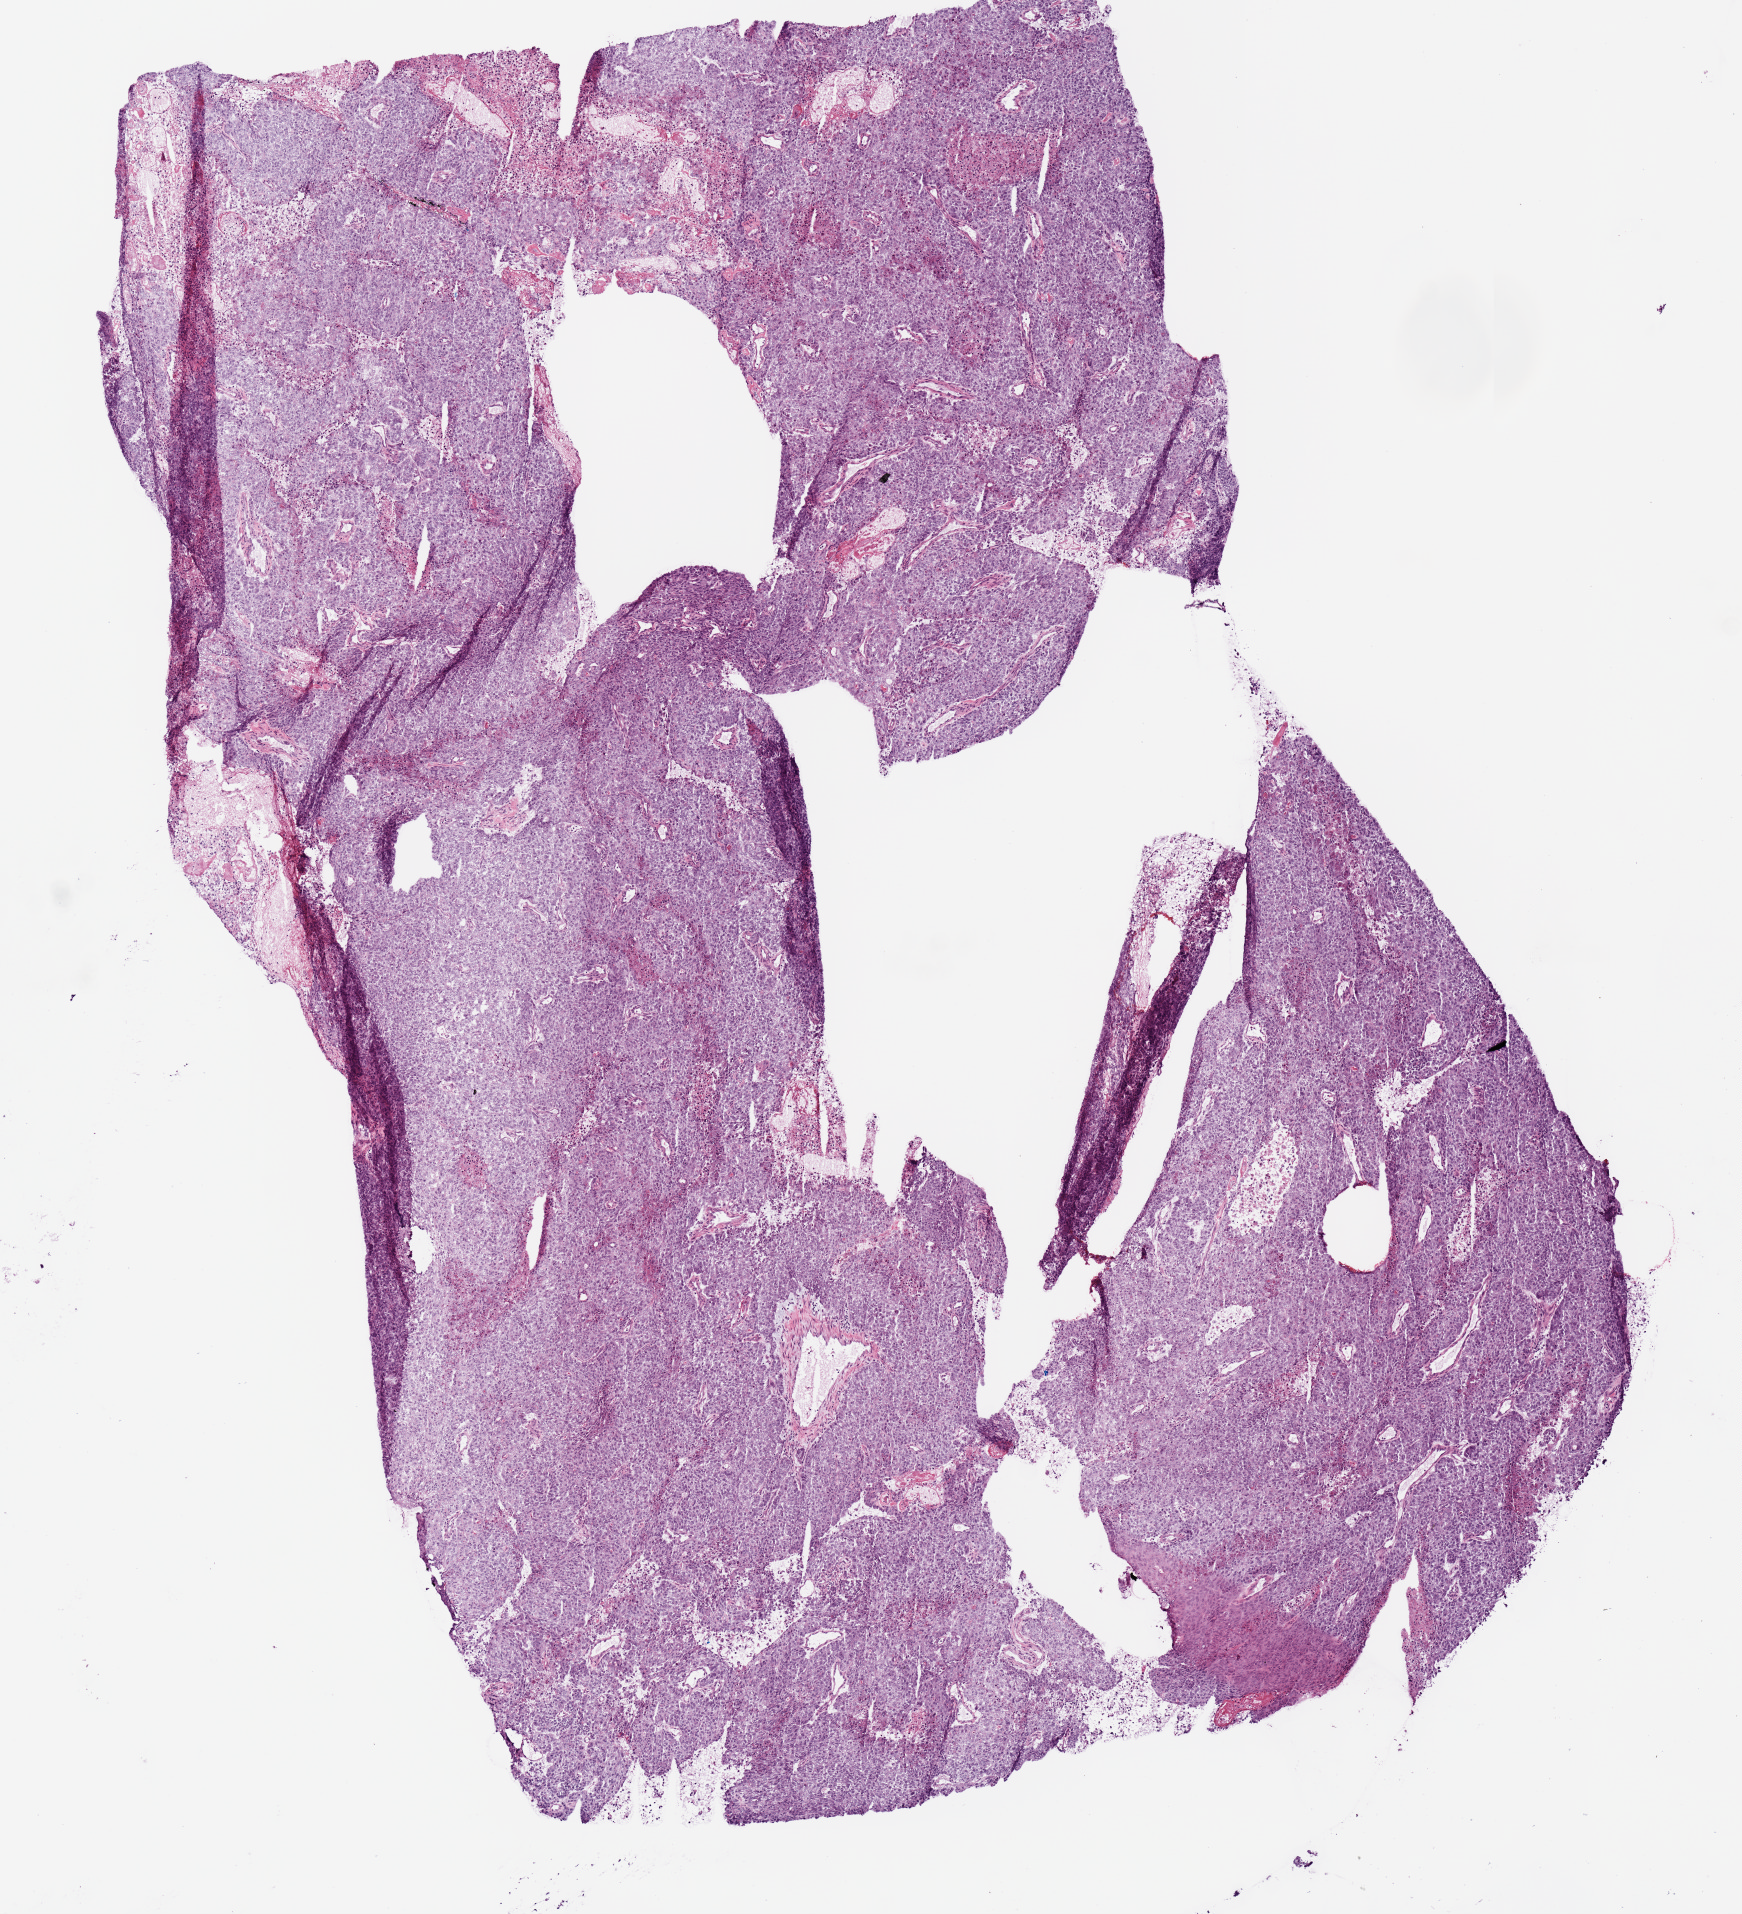
Whole-slide histology image, H&E, shown as a low-resolution overview of the whole scanned area (about 6.9 x 7.6 mm, slide scanned at 20x), frozen section from the top of the tissue portion, sample: primary tumour, uterus. Female, age 63 years at initial diagnosis. Histologic grade: G3 (poorly differentiated). Slide review estimates, as recorded: tumour cells 92%, tumour nuclei 85%, normal cells 0%, stromal cells 5%, necrosis 8%. Infiltration values recorded for this section: lymphocyte infiltration 0%, monocyte infiltration 0%, neutrophil infiltration 0%.
- pathologic diagnosis: Endometrioid adenocarcinoma, NOS
- FIGO stage: IA
- lymph nodes positive (case pathology): 0 of 12 examined